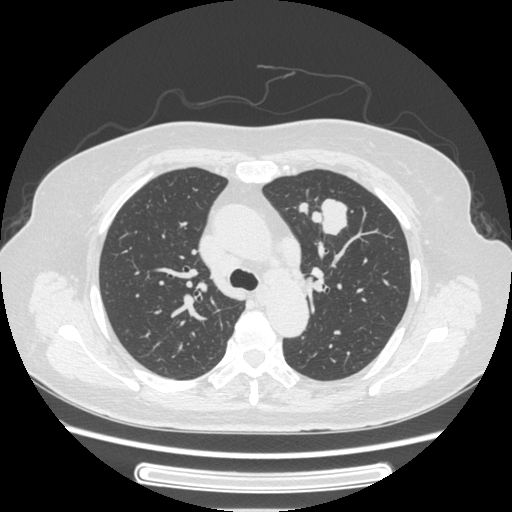
Chest CT, one axial slice. Lung window (W 1500 / L -600 HU). 1.25 mm slice thickness. 512 × 512 image matrix, field of view 363 × 363 mm. Patient: female, 77 years. From the clinical record (not read from this slice): clinical TNM (as recorded): T1c N3 M0; histopathological grade: G2-3.
Annotated regions visible in this slice (rectangle marked by the reading radiologist):
- lung tumour (recorded histology: adenocarcinoma): box from (x=298, y=195) to (x=356, y=240) px